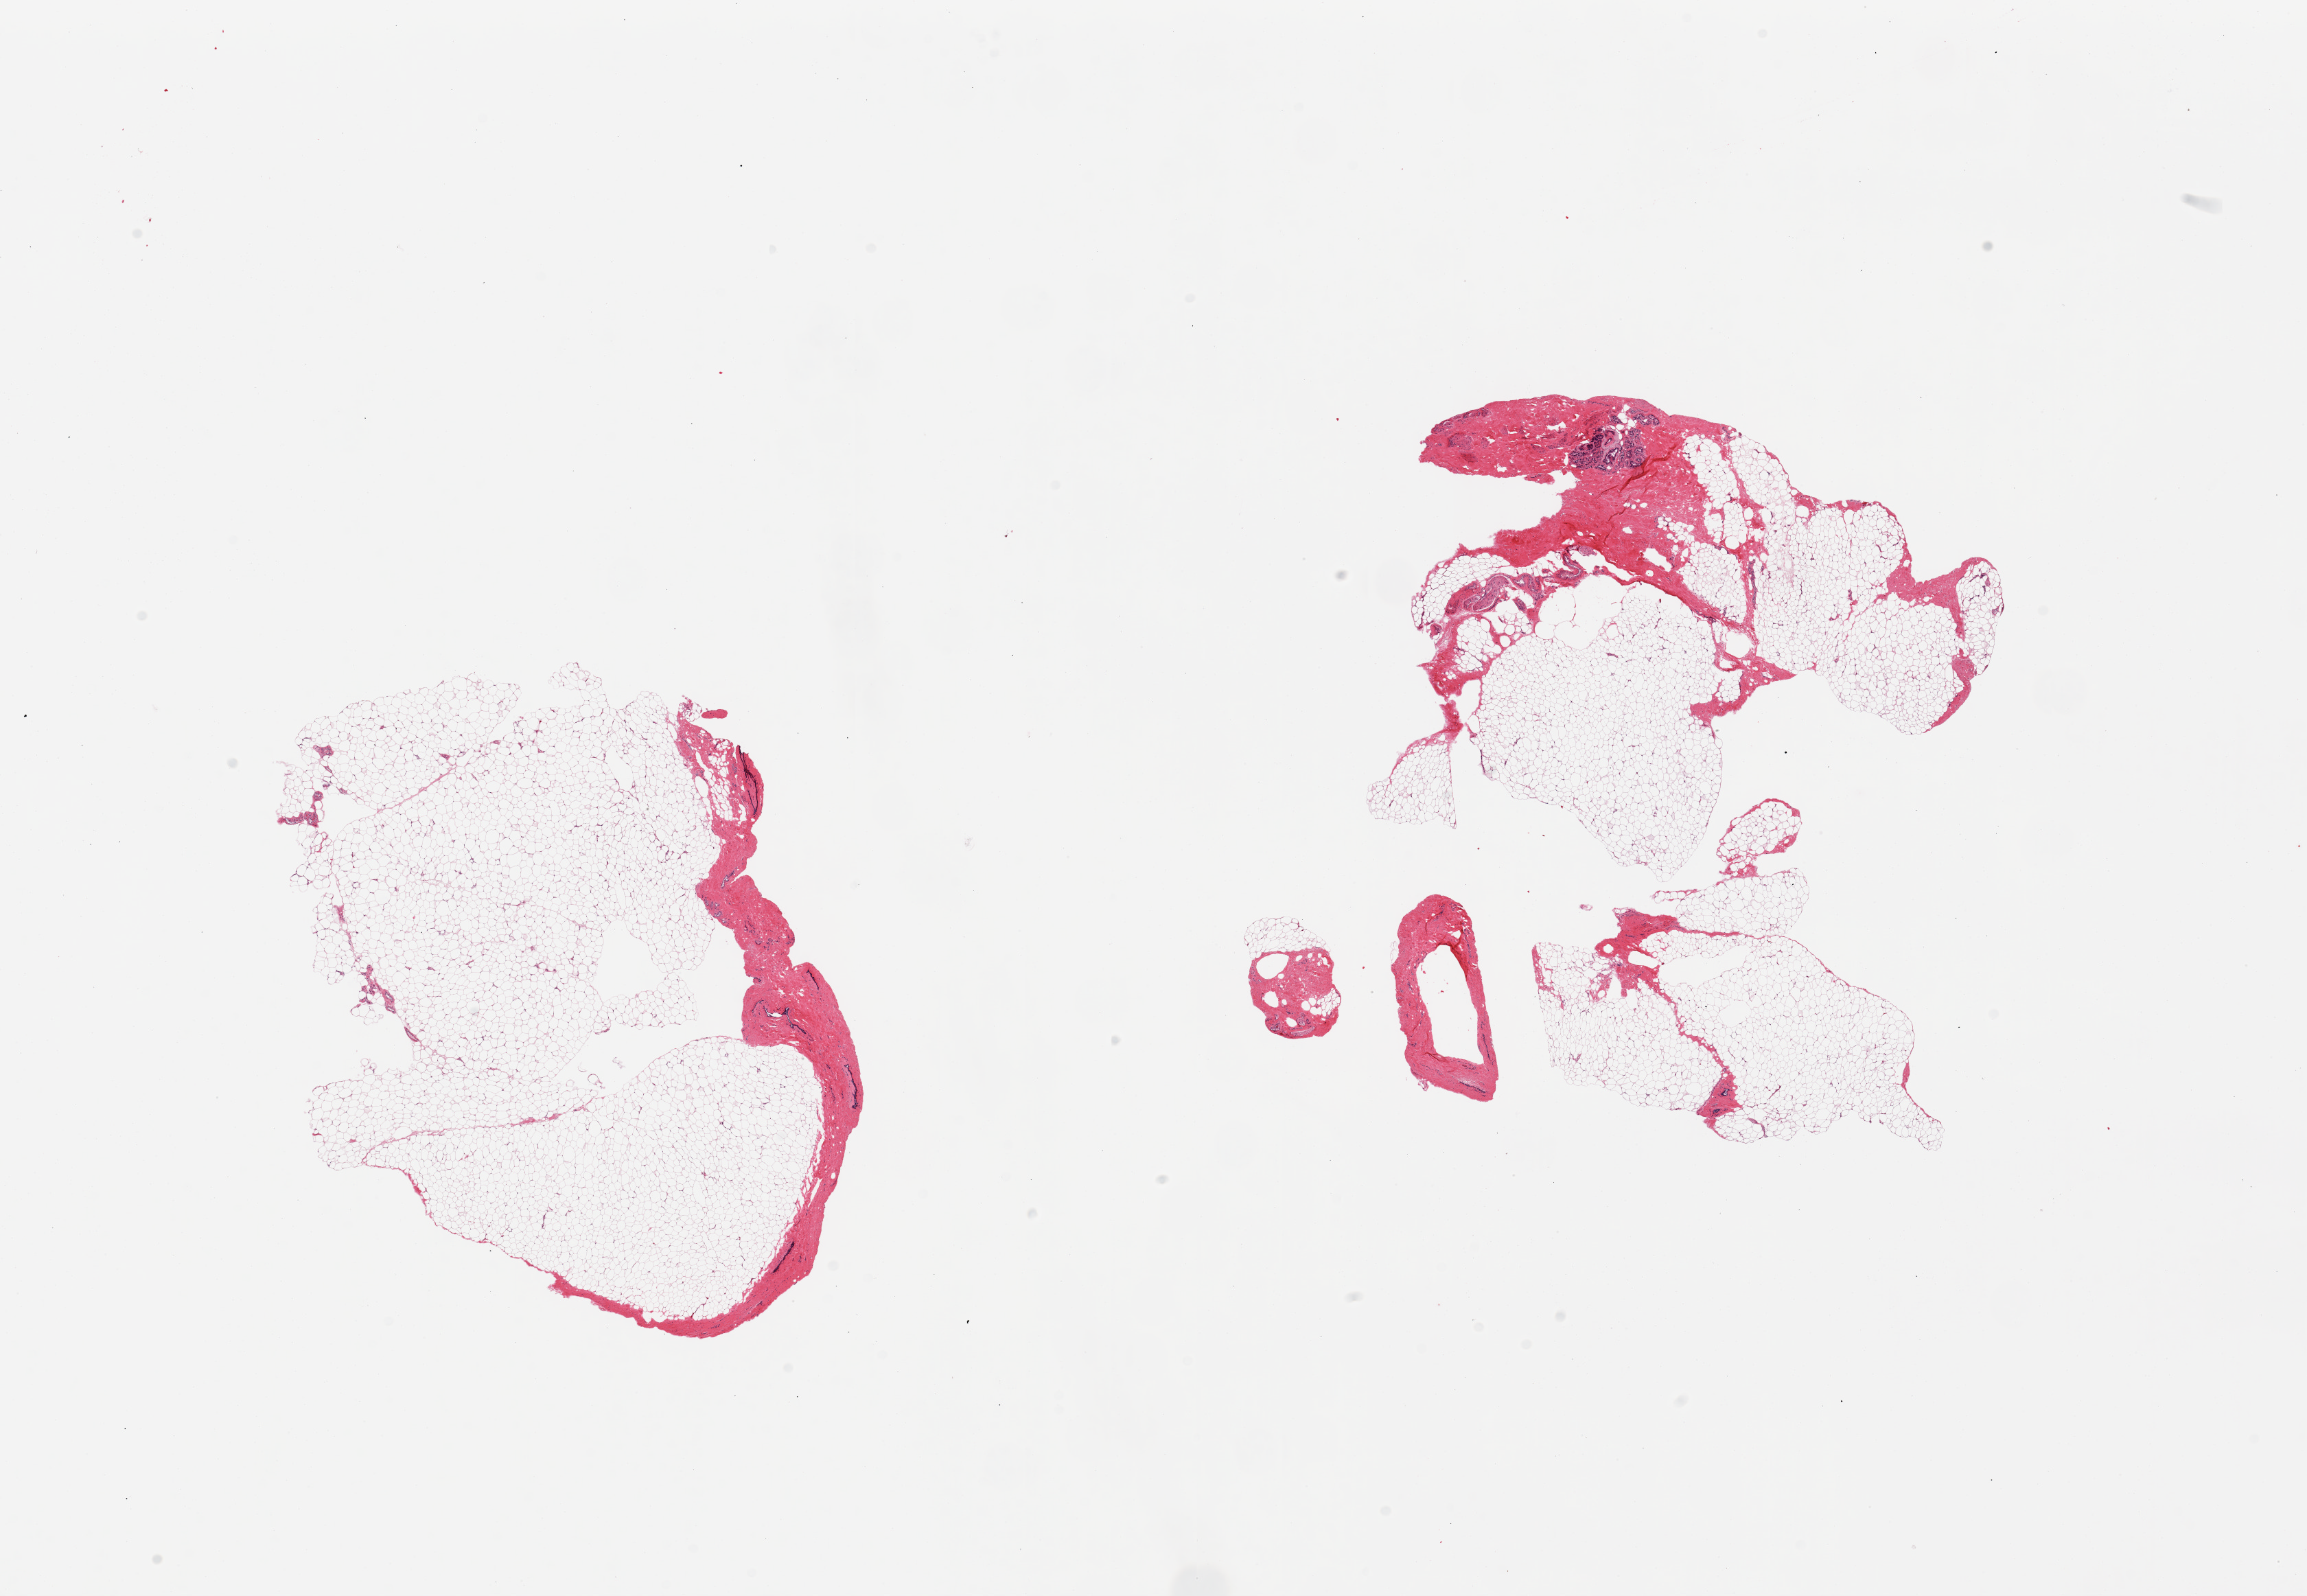
Digitized haematoxylin and eosin-stained section, brightfield, a low-resolution overview of the entire scanned area, about 26.6 x 18.4 mm (acquisition: 20x scan). PAXgene-fixed paraffin-embedded (PFPE) section. Target tissue: breast. Donor tissue sample. Donor: male.
Review note (as recorded): 2 pieces; mature adipose tissue and up to 20% fibrovascular component; focus of autolyzed ductal structures.